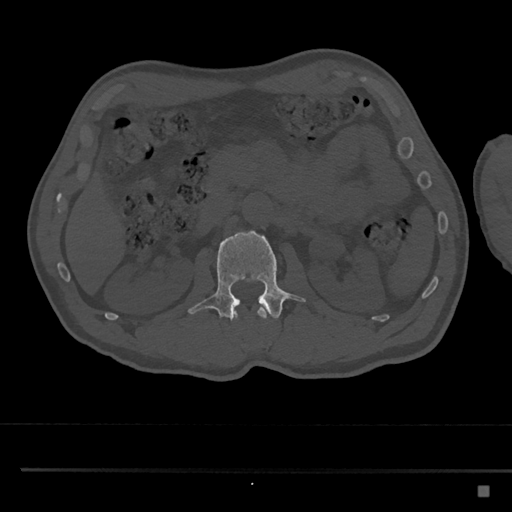
CT including the spine, one axial slice. Position 774 of 797 along the scan axis. 120 kVp. Bone window (W 1800 / L 400 HU). 512 × 512 image matrix, field of view 391 × 391 mm. Patient: male, 59 years. From the clinical record (not read from this slice): primary cancer: prostate.
Outlined on this slice (semi-automatically segmented with operator editing):
- L1 vertebra: bounding box (x1, y1, x2, y2) in pixels: (231, 307, 267, 319)
- L2 vertebra: (188, 230, 307, 320)